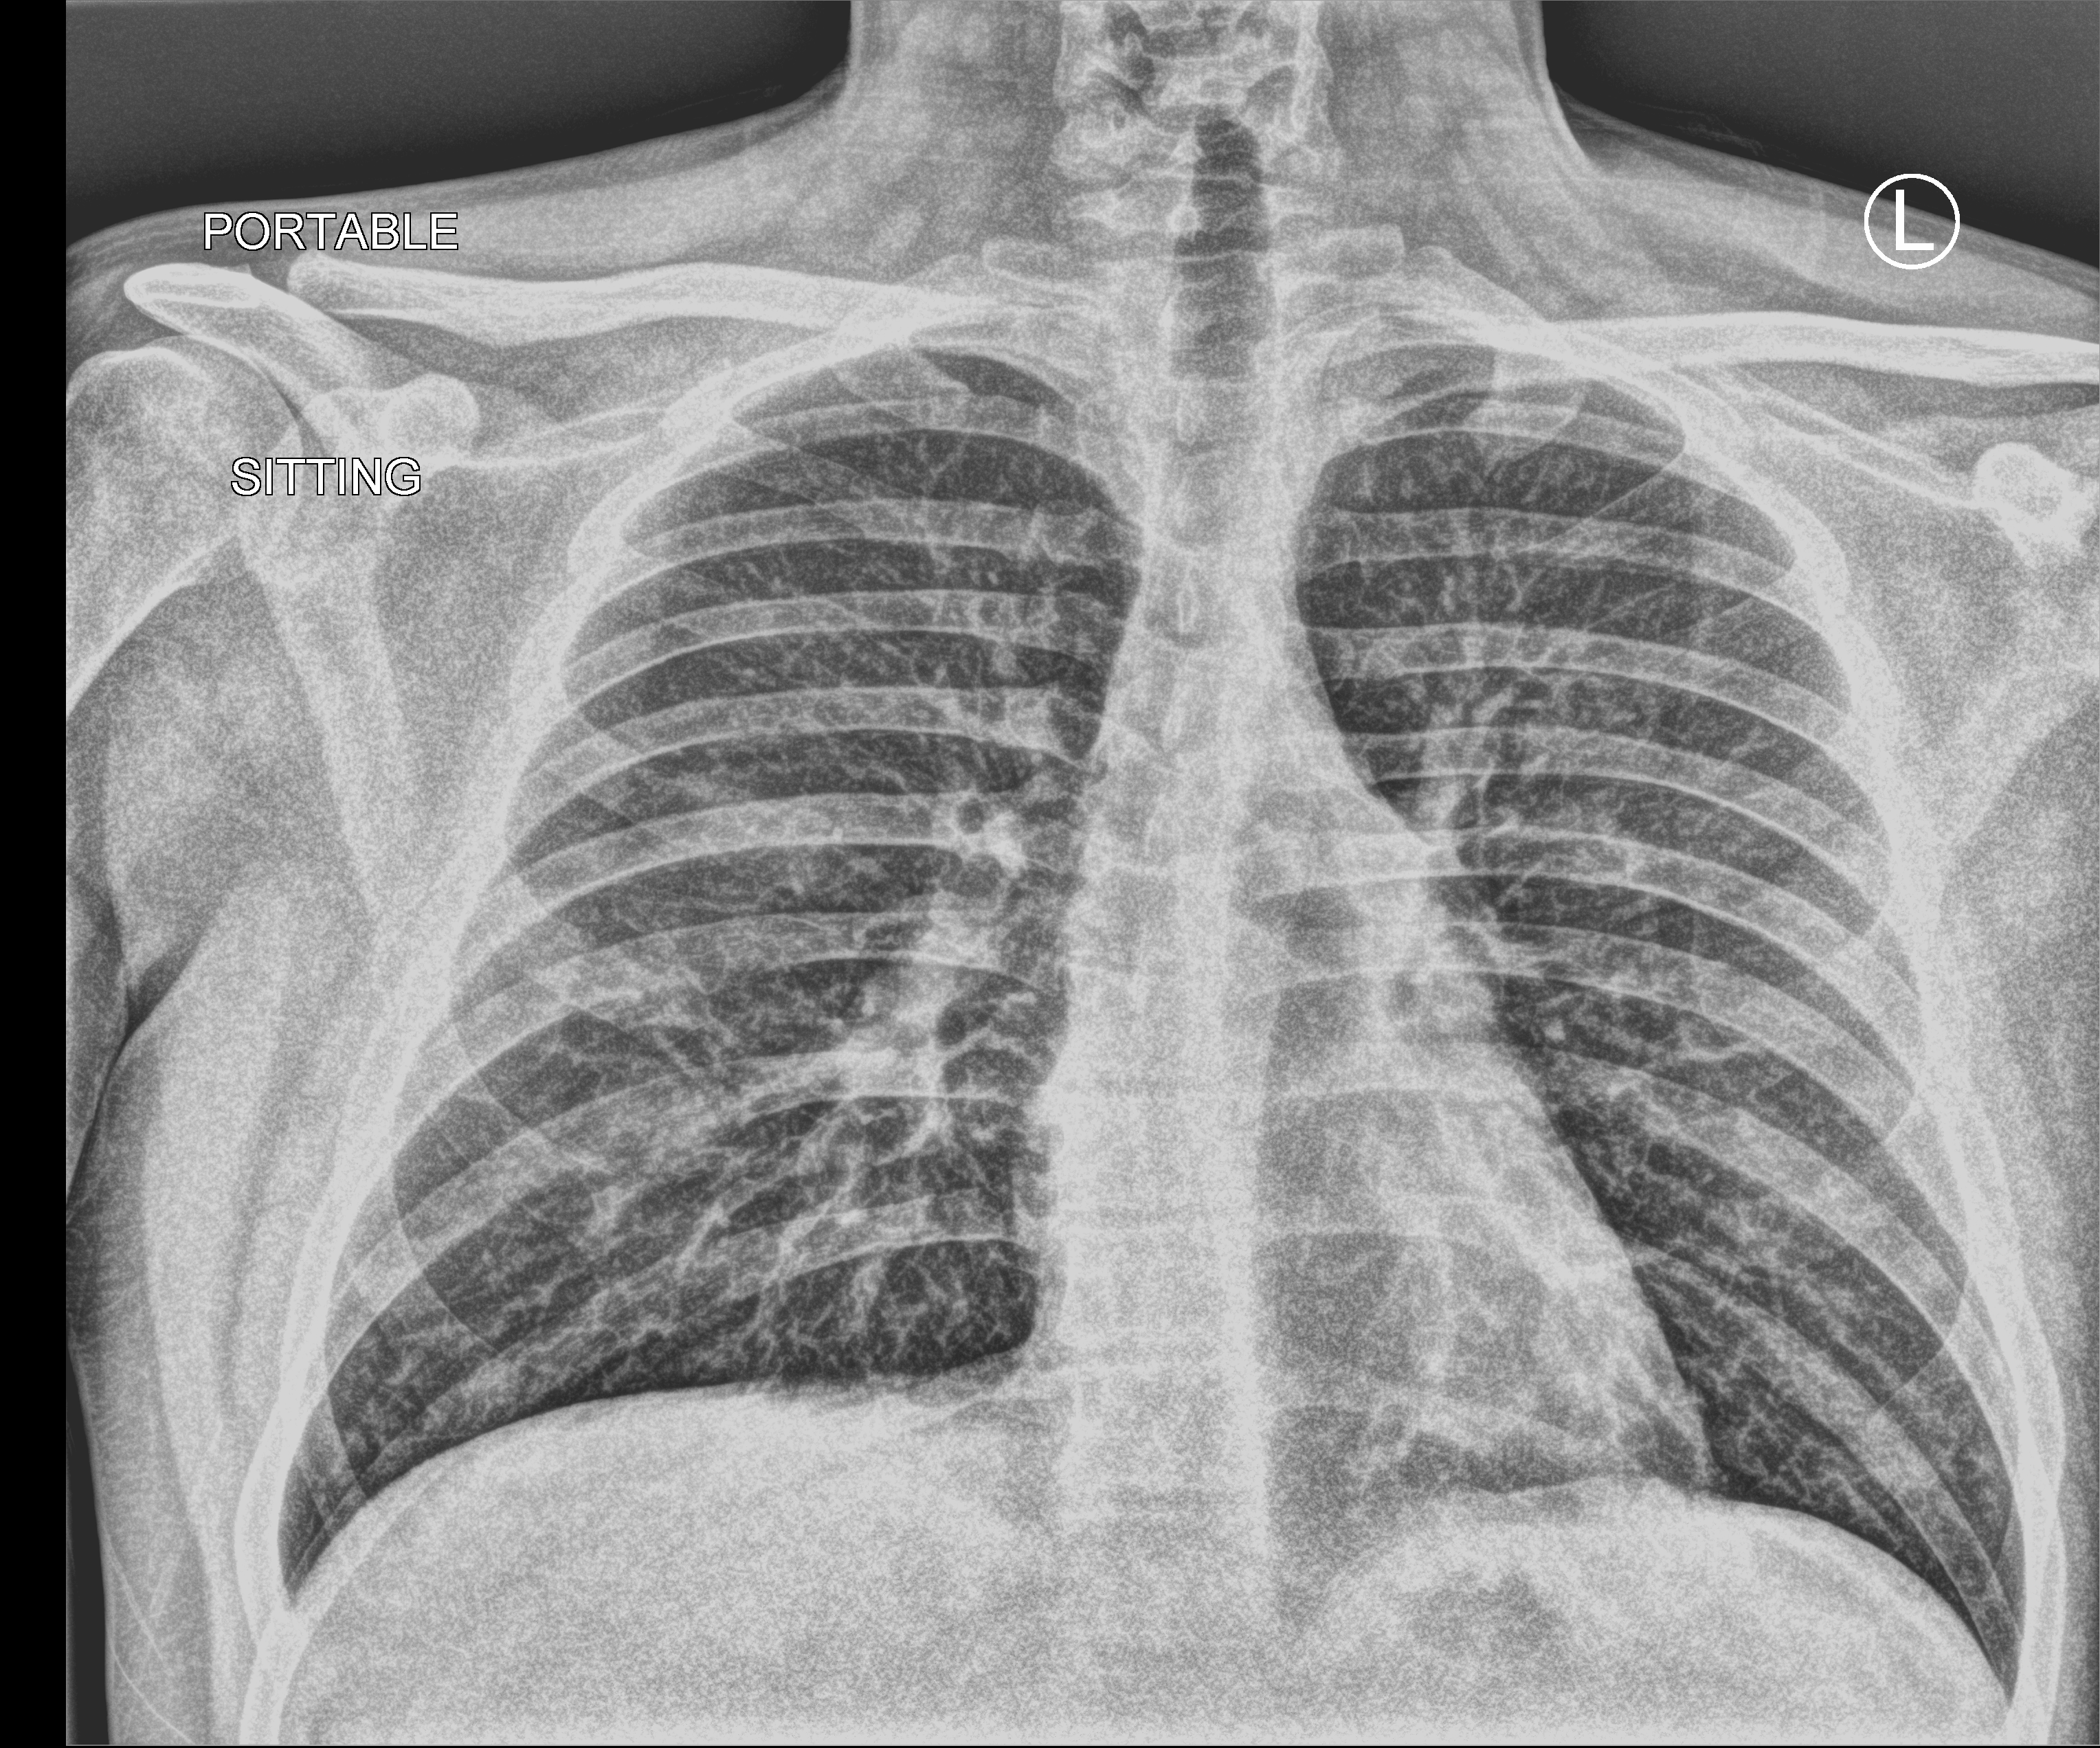
Portable chest radiograph. Male patient hospitalised with COVID-19, age 18–59 years.
From the hospital-stay record, not from the radiograph (when in the stay this image was taken is not recorded):
- mechanically ventilated during this hospital stay: no
- length of hospital stay: 1 day
- admitted to intensive care during this hospital stay: no